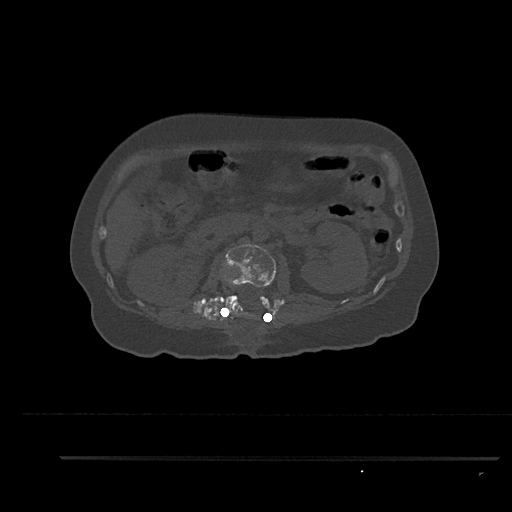
CT including the spine, one axial slice; slice 185 of 797 in the series (ordered by position); 120 kVp; bone window (W 1800 / L 400 HU); 512 × 512 image matrix, field of view 408 × 408 mm. Patient: female, 44 years. From the clinical record (not read from this slice): primary cancer: renal.
Structures marked on this image (semi-automatically segmented with operator editing):
- L1 vertebra: bounding box [x1, y1, x2, y2] px = [232, 284, 239, 309]
- L2 vertebra: [224, 244, 276, 319]